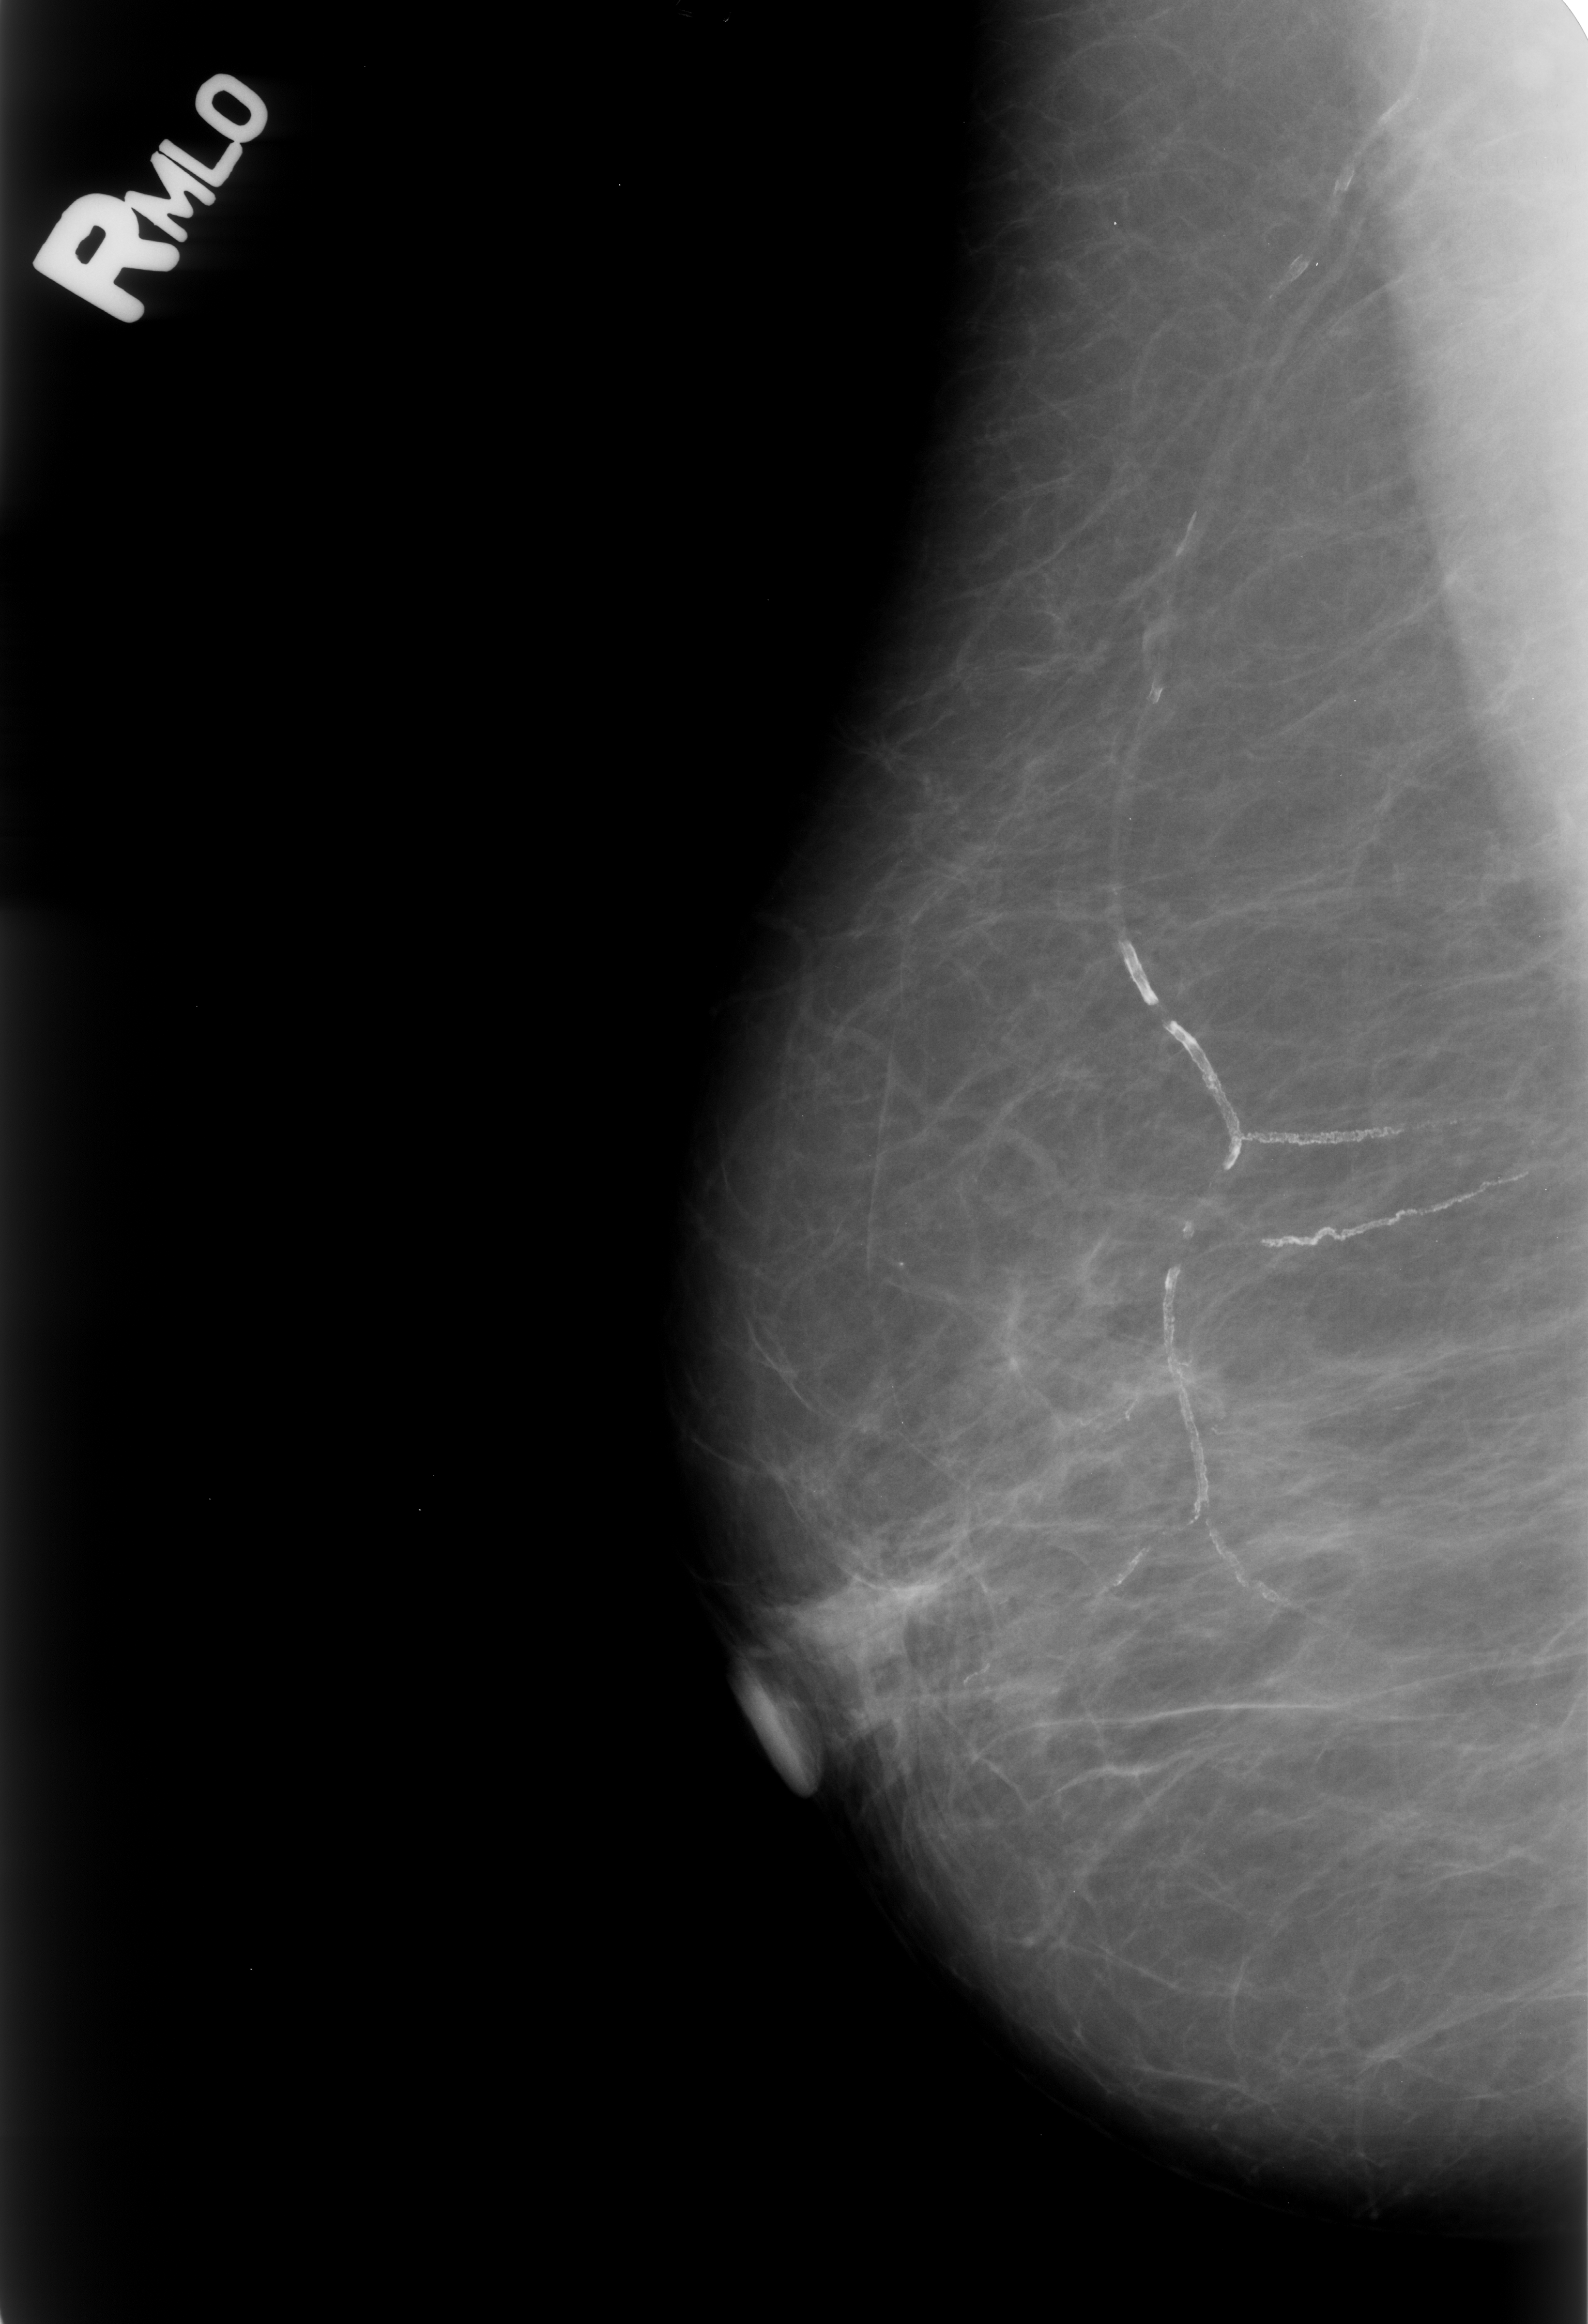
Mammogram (digitized film). Right breast. Mediolateral oblique (MLO) view. Breast composition: almost entirely fatty (BI-RADS density category 1 of 4). 1588 × 2324 image matrix.
Marked abnormalities (boxes around the expert regions of interest):
- Finding 1 of 5: calcifications, morphology fine linear branching; BI-RADS assessment category 2; outcome (as recorded, no biopsy): benign without callback (not worked up further): bounding box (x1, y1, x2, y2) in pixels: (1033, 1348, 1105, 1424)
- Finding 2 of 5: calcifications, morphology vascular; BI-RADS assessment category 2; outcome (as recorded, no biopsy): benign without callback (not worked up further): (1046, 479, 1345, 1688)
- Finding 3 of 5: calcifications, morphology fine linear branching; BI-RADS assessment category 2; subtlety rating 4 on a 1 (subtle) to 5 (obvious) scale; outcome (as recorded, no biopsy): benign without callback (not worked up further): (1104, 1368, 1159, 1464)
- Finding 4 of 5: calcifications, morphology vascular; BI-RADS assessment category 2; benign; no additional work-up was recommended (outcome (as recorded, no biopsy): benign without callback): (1244, 1091, 1461, 1171)
- Finding 5 of 5: calcifications, morphology vascular; BI-RADS assessment category 2; outcome (as recorded, no biopsy): benign without callback (not worked up further): (1244, 1157, 1544, 1275)